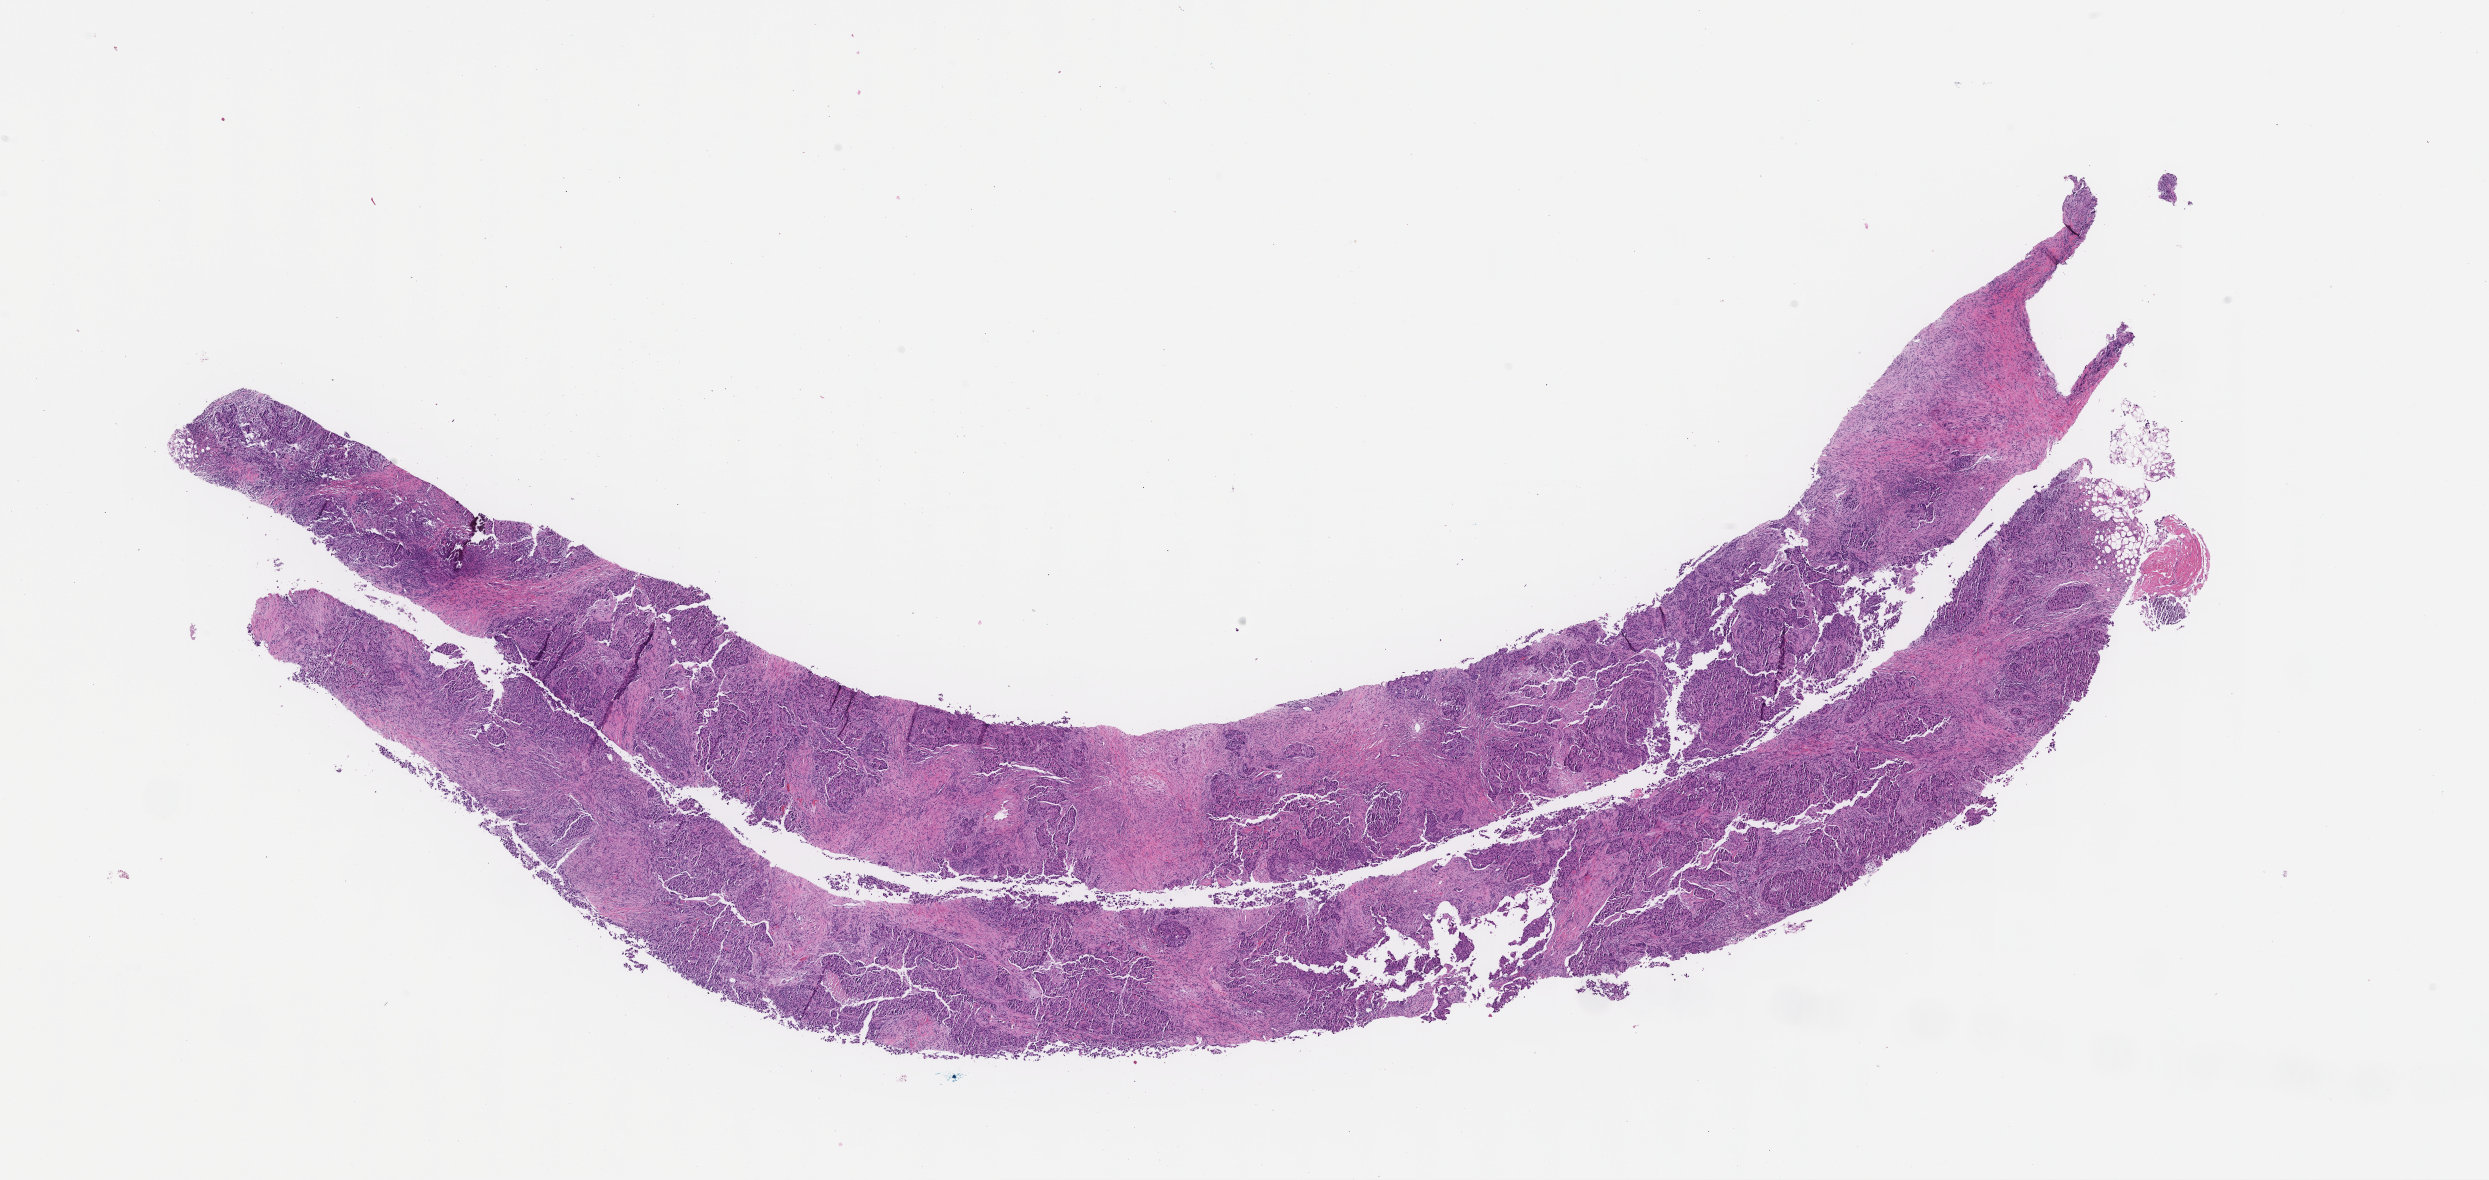
Whole-slide image, H&E stain — a low-resolution overview of the entire scanned area, about 20.1 x 9.5 mm. FFPE section. Tissue site: breast. Specimen time point: archival tissue. Patient: female.
This section: primary tumor. Diagnosis: Invasive Breast Carcinoma.